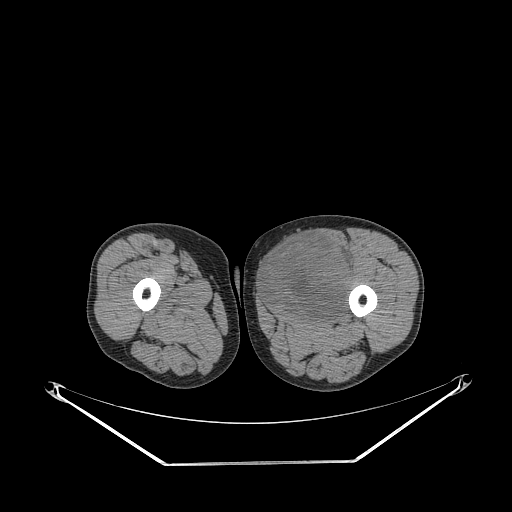
CT of an extremity soft-tissue mass (from a PET/CT study), one axial slice. Slice 246 of 267 in the series (ordered by position). Reconstruction kernel STANDARD. Soft-tissue window (W 400 / L 40 HU). 512 × 512 image matrix, field of view 500 × 500 mm. Male patient. Case-level facts recorded for this patient, not image findings: histological type: pleiomorphic liposarcoma; grade: high; site of the primary tumour: left thigh.
Structures marked on this image (expert contour drawn on MRI and transferred to this co-registered scan by the dataset authors):
- gross tumour volume including surrounding oedema: bounding box <263,233,355,318> (left, top, right, bottom; pixels)
- gross tumour volume (mass): <263,233,352,320>